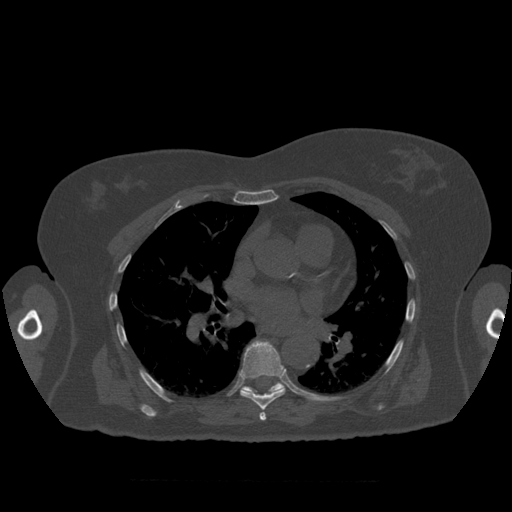
CT including the spine, one axial slice. Position 392 of 399 along the scan axis. Reconstruction kernel STANDARD. 120 kVp. Bone window (W 1800 / L 400 HU). 512 × 512 image matrix, field of view 404 × 404 mm. Patient age 81 years. From the clinical record (not read from this slice): primary cancer: renal; vertebrae with lytic lesions (as recorded): L1.
Outlined on this slice (semi-automatically segmented with operator editing):
- T7 vertebra: box from (x=240, y=341) to (x=286, y=421) px
- T8 vertebra: (x=241, y=381)–(x=285, y=394)